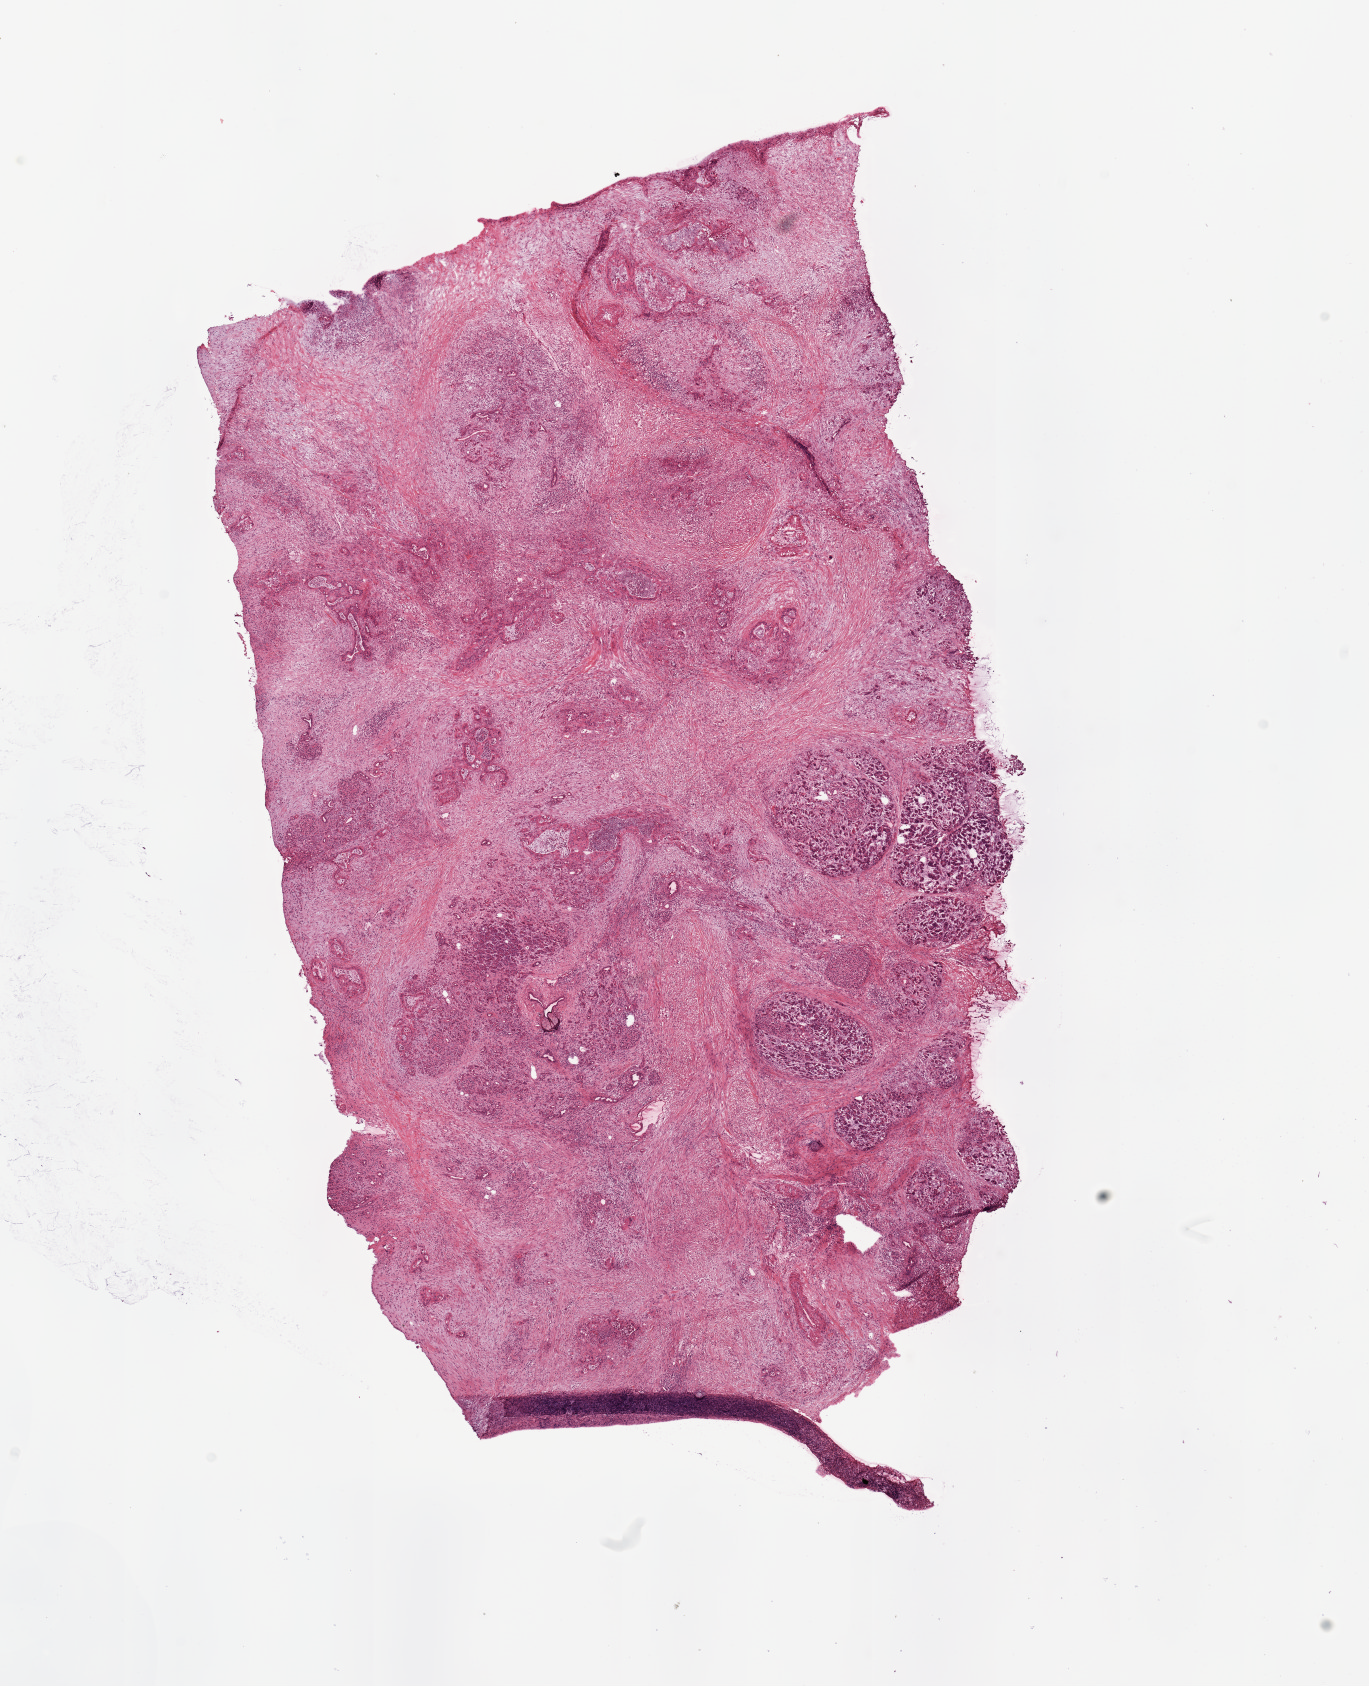
H&E-stained whole-slide image — shown as a low-resolution overview of the whole scanned area (about 10.8 x 13.3 mm). Tumour tissue sample, sampled site: pancreas. Female, 62 y/o. Histologic grade: G2 (moderately differentiated). Slide review estimates, as recorded: tumour nuclei 15%, necrosis 2%.
Primary tumour site (as recorded): body. AJCC pathologic stage: IIB. Diagnosis: Infiltrating duct carcinoma, NOS.